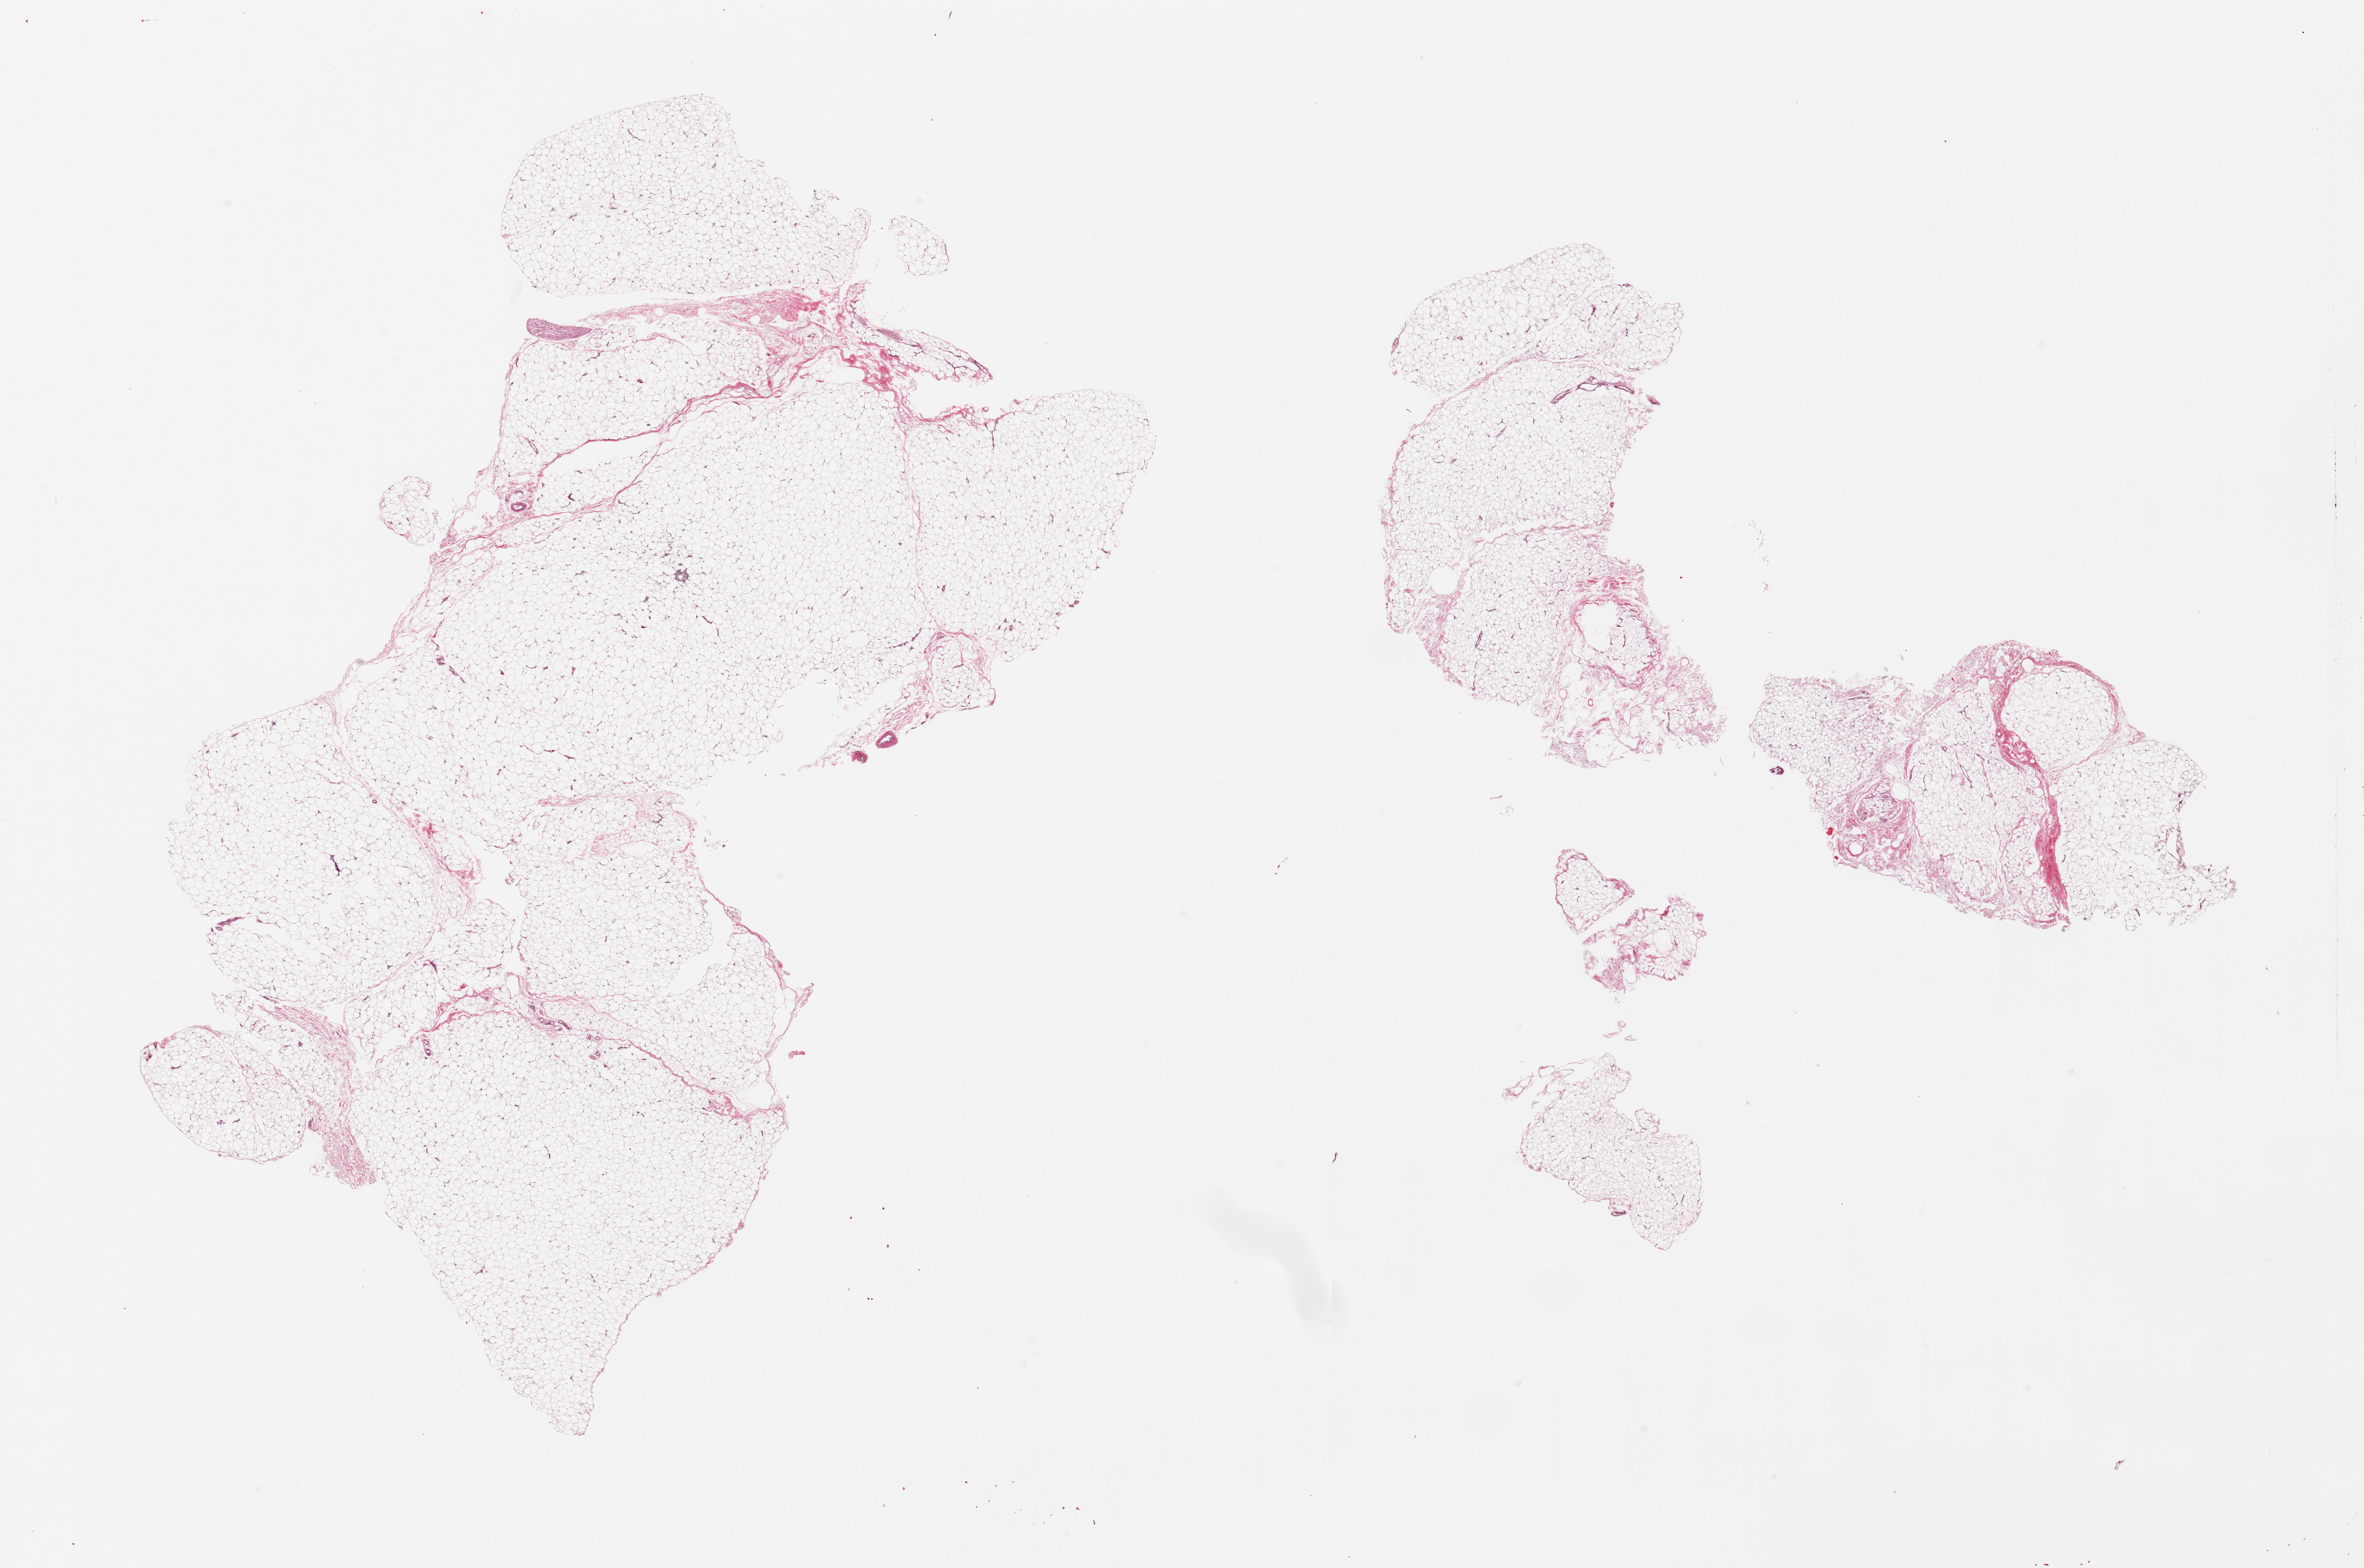
Digitized hematoxylin and eosin (H&E)-stained section — shown as a low-resolution overview of the whole scanned area (about 31.5 x 20.9 mm), PAXgene-fixed, paraffin-embedded tissue, target tissue: adipose tissue, donor tissue sample. Donor sex: female.
- reviewer comment on this tissue sample: 2 pieces, trace fascia